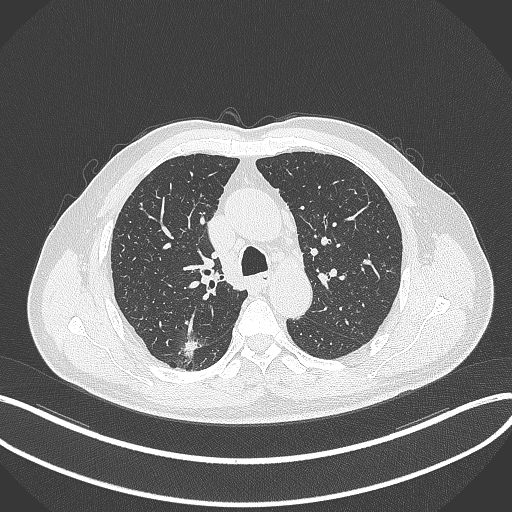
Chest CT, one axial slice; slice 255 of 359 in the series (ordered by position); reconstruction kernel B70f; 120 kVp; lung window (W 1500 / L -600 HU); 1 mm slice thickness; 512 × 512 image matrix. Male patient, age 69 years. From the clinical record (not read from this slice): clinical TNM (as recorded): T1b N0 M0.
Structures marked on this image (rectangle marked by the reading radiologist):
- lung tumour (recorded histology: adenocarcinoma): bounding box [x1, y1, x2, y2] px = [178, 339, 202, 364]